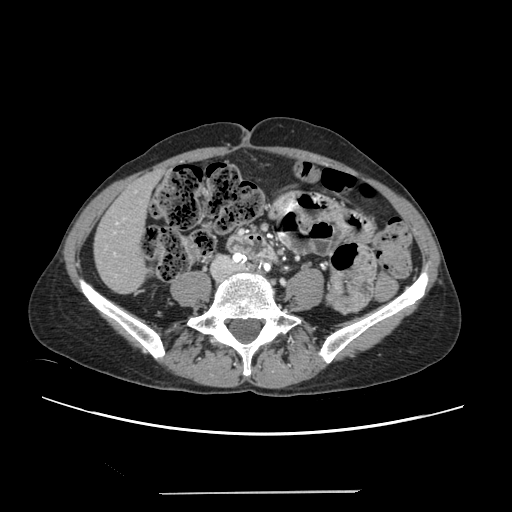
Contrast-enhanced abdominal CT, one axial slice; slice 37 of 240 in the series (ordered by position); intravenous contrast given; soft-tissue window (W 400 / L 40 HU); 512 × 512 image matrix, field of view 371 × 371 mm. Female patient, age 60 years. From the clinical record (not read from this slice): diagnosis: colorectal cancer liver metastases, imaged before liver resection; multiple liver metastases: no; largest metastasis: 1.5 cm; chemotherapy before resection: yes.
Annotated regions visible in this slice (expert manual segmentation):
- liver: bounding box [x1, y1, x2, y2] px = [95, 174, 157, 293]
- planned liver remnant (the part of the liver to remain after resection): [95, 175, 158, 293]
- portal vein (with intrahepatic branches): [114, 217, 125, 255]